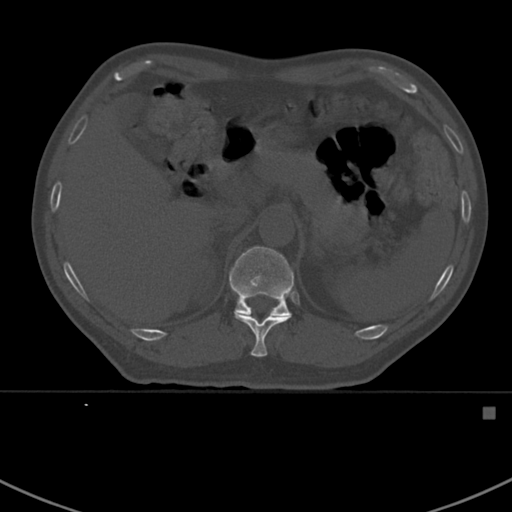
CT including the spine, one axial slice. Position 339 of 412 along the scan axis. Reconstruction kernel Br40s. 120 kVp. Bone window (W 1800 / L 400 HU). 1.5 mm slice thickness. 512 × 512 image matrix. Patient: male, 59 years. From the clinical record (not read from this slice): primary cancer: prostate.
Structures marked on this image (semi-automatically segmented with operator editing):
- T11 vertebra: bounding box <234,313,291,357> (left, top, right, bottom; pixels)
- T12 vertebra: <229,246,294,316>